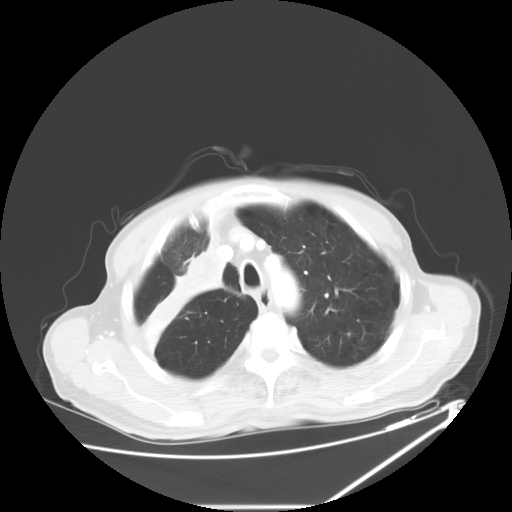
Chest CT, one axial slice; 120 kVp; lung window (W 1500 / L -600 HU); 5 mm slice thickness; 512 × 512 image matrix, field of view 410 × 410 mm. Patient: male, 73 years. Case-level facts recorded for this patient, not image findings: clinical TNM (as recorded): T2a N1 M0.
Annotated regions visible in this slice (bounding box drawn by a radiologist):
- lung tumour (recorded histology: squamous cell carcinoma): bounding box (x1, y1, x2, y2) in pixels: (142, 241, 228, 356)